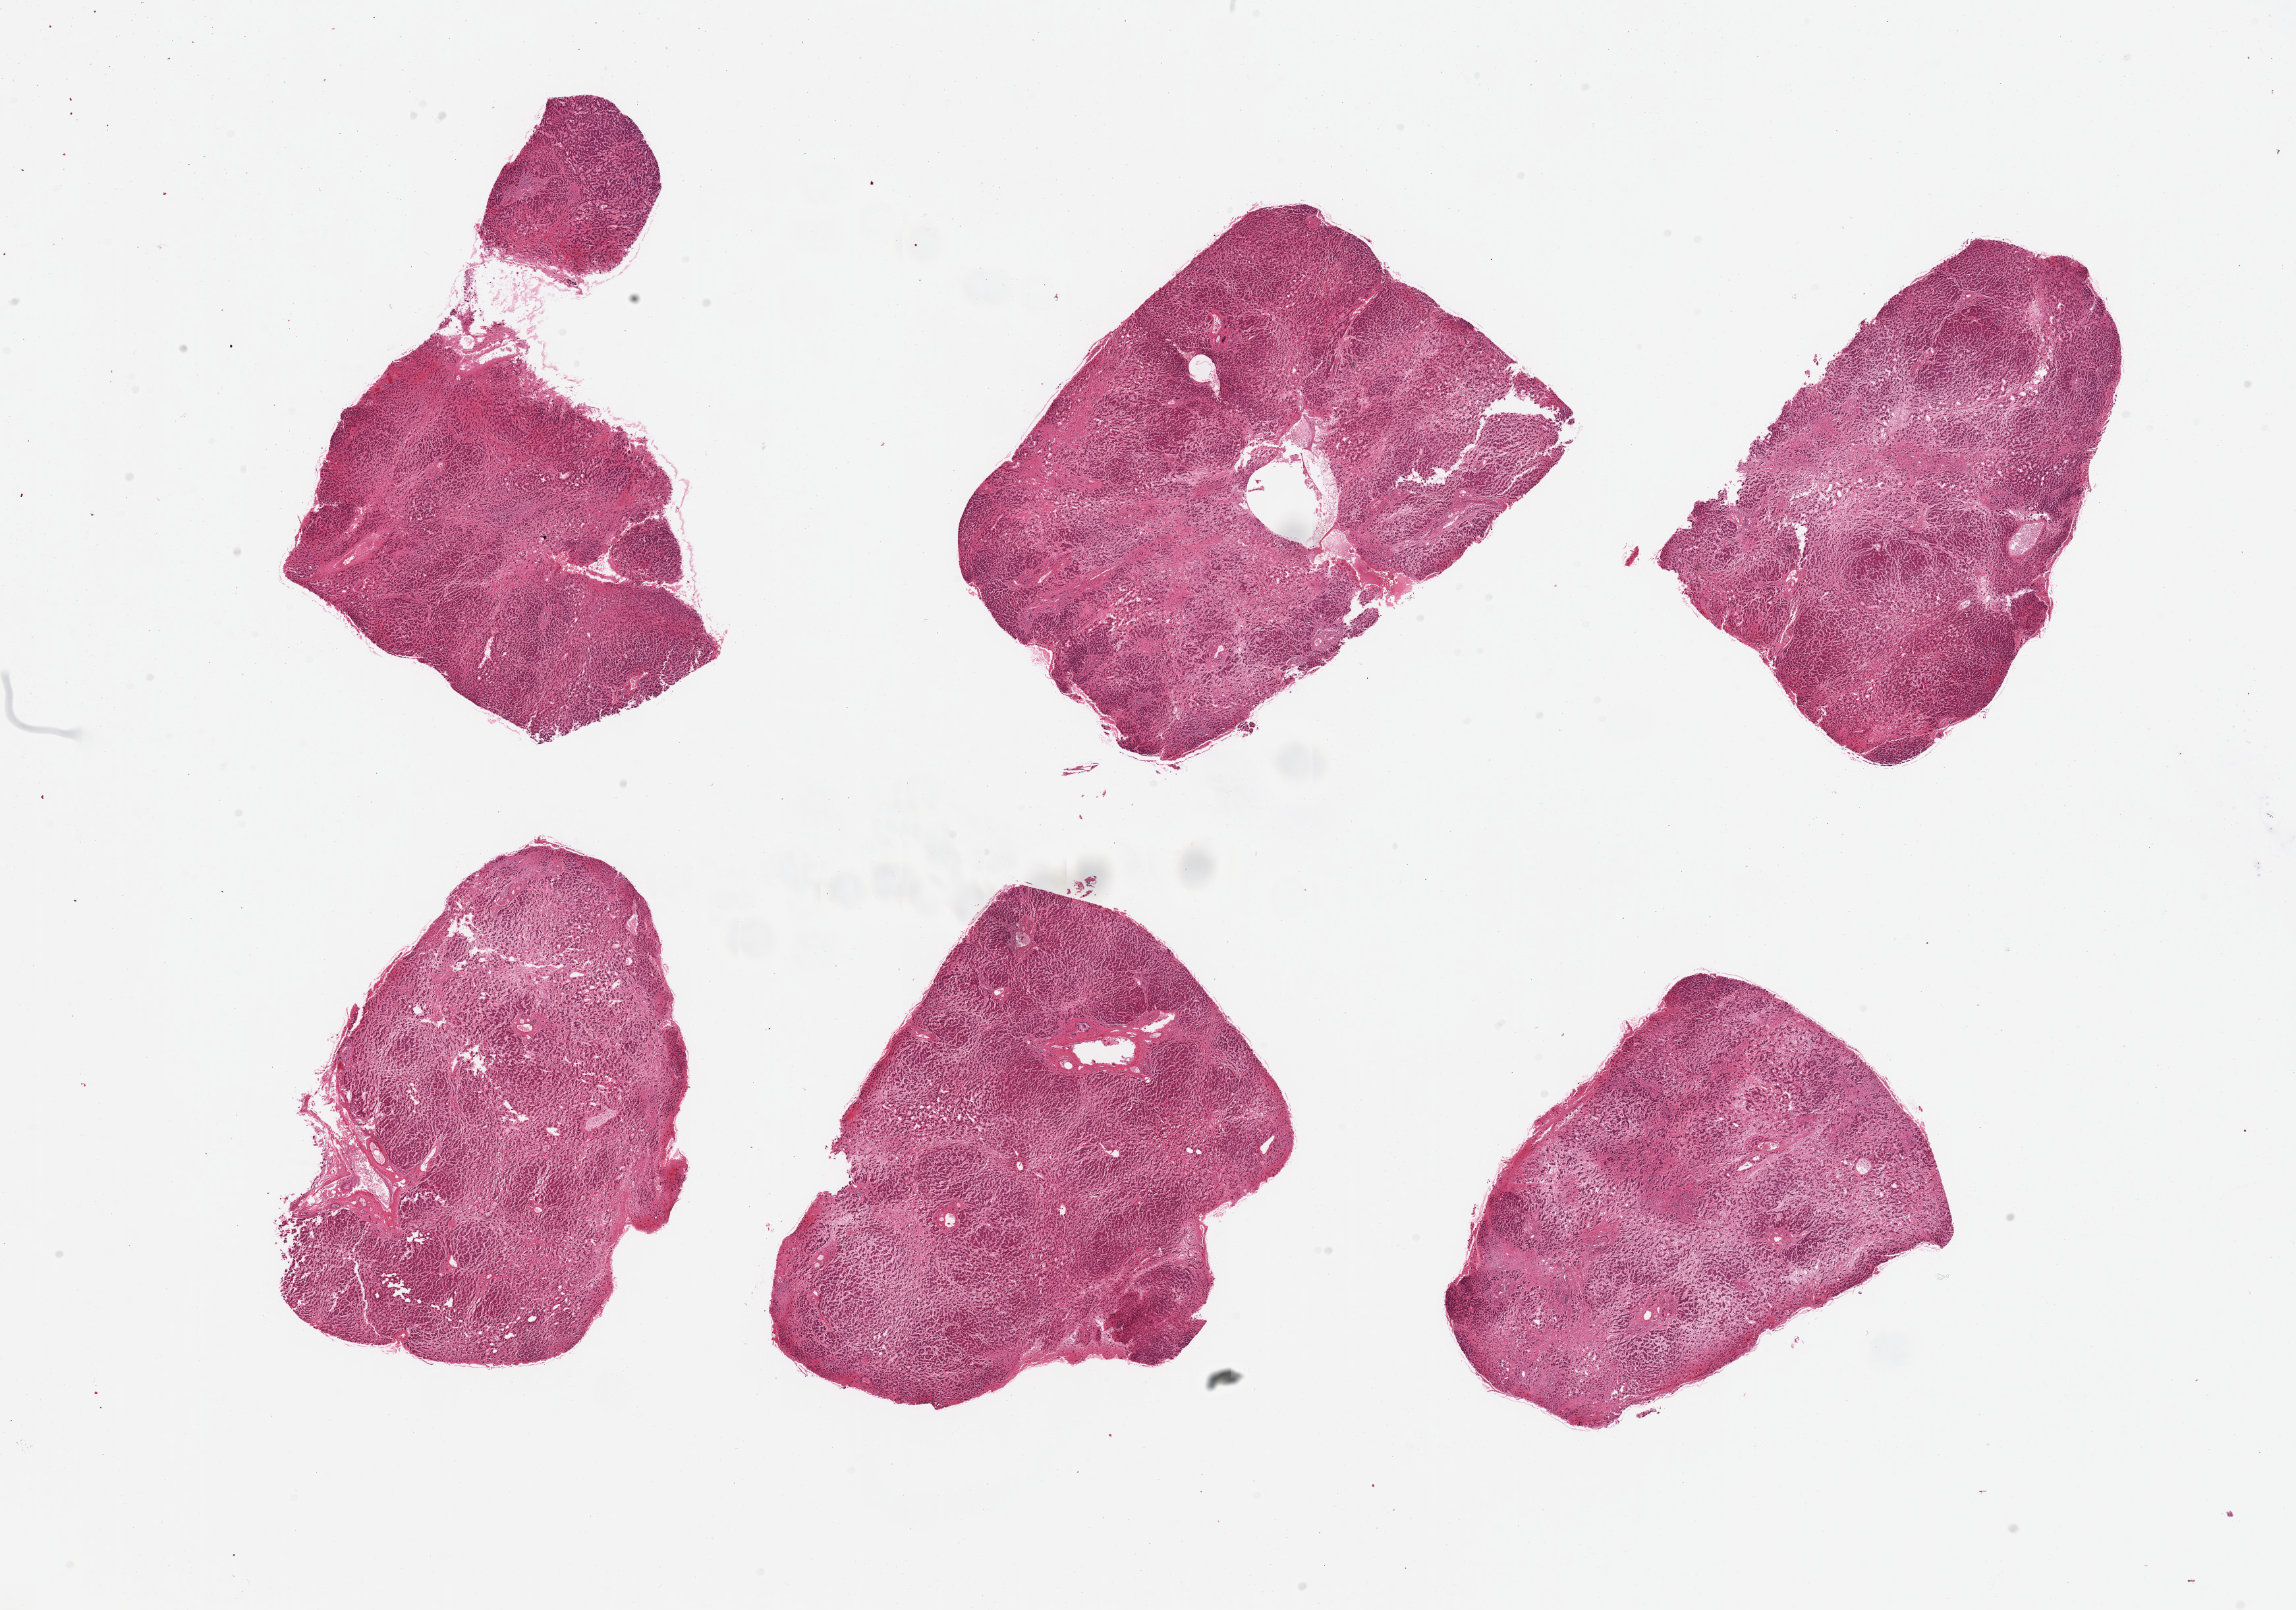
Whole-slide image, H&E stain — a low-resolution overview of the entire scanned area, about 27.6 x 19.3 mm (from a 20x scan); PAXgene-fixed paraffin-embedded (PFPE) section; sampled site (target tissue): renal cortex; tissue donor sample. Donor: male.
Pathologist's review note for this sample: 6 pieces; renal cortex not present; cirrhotic liver.